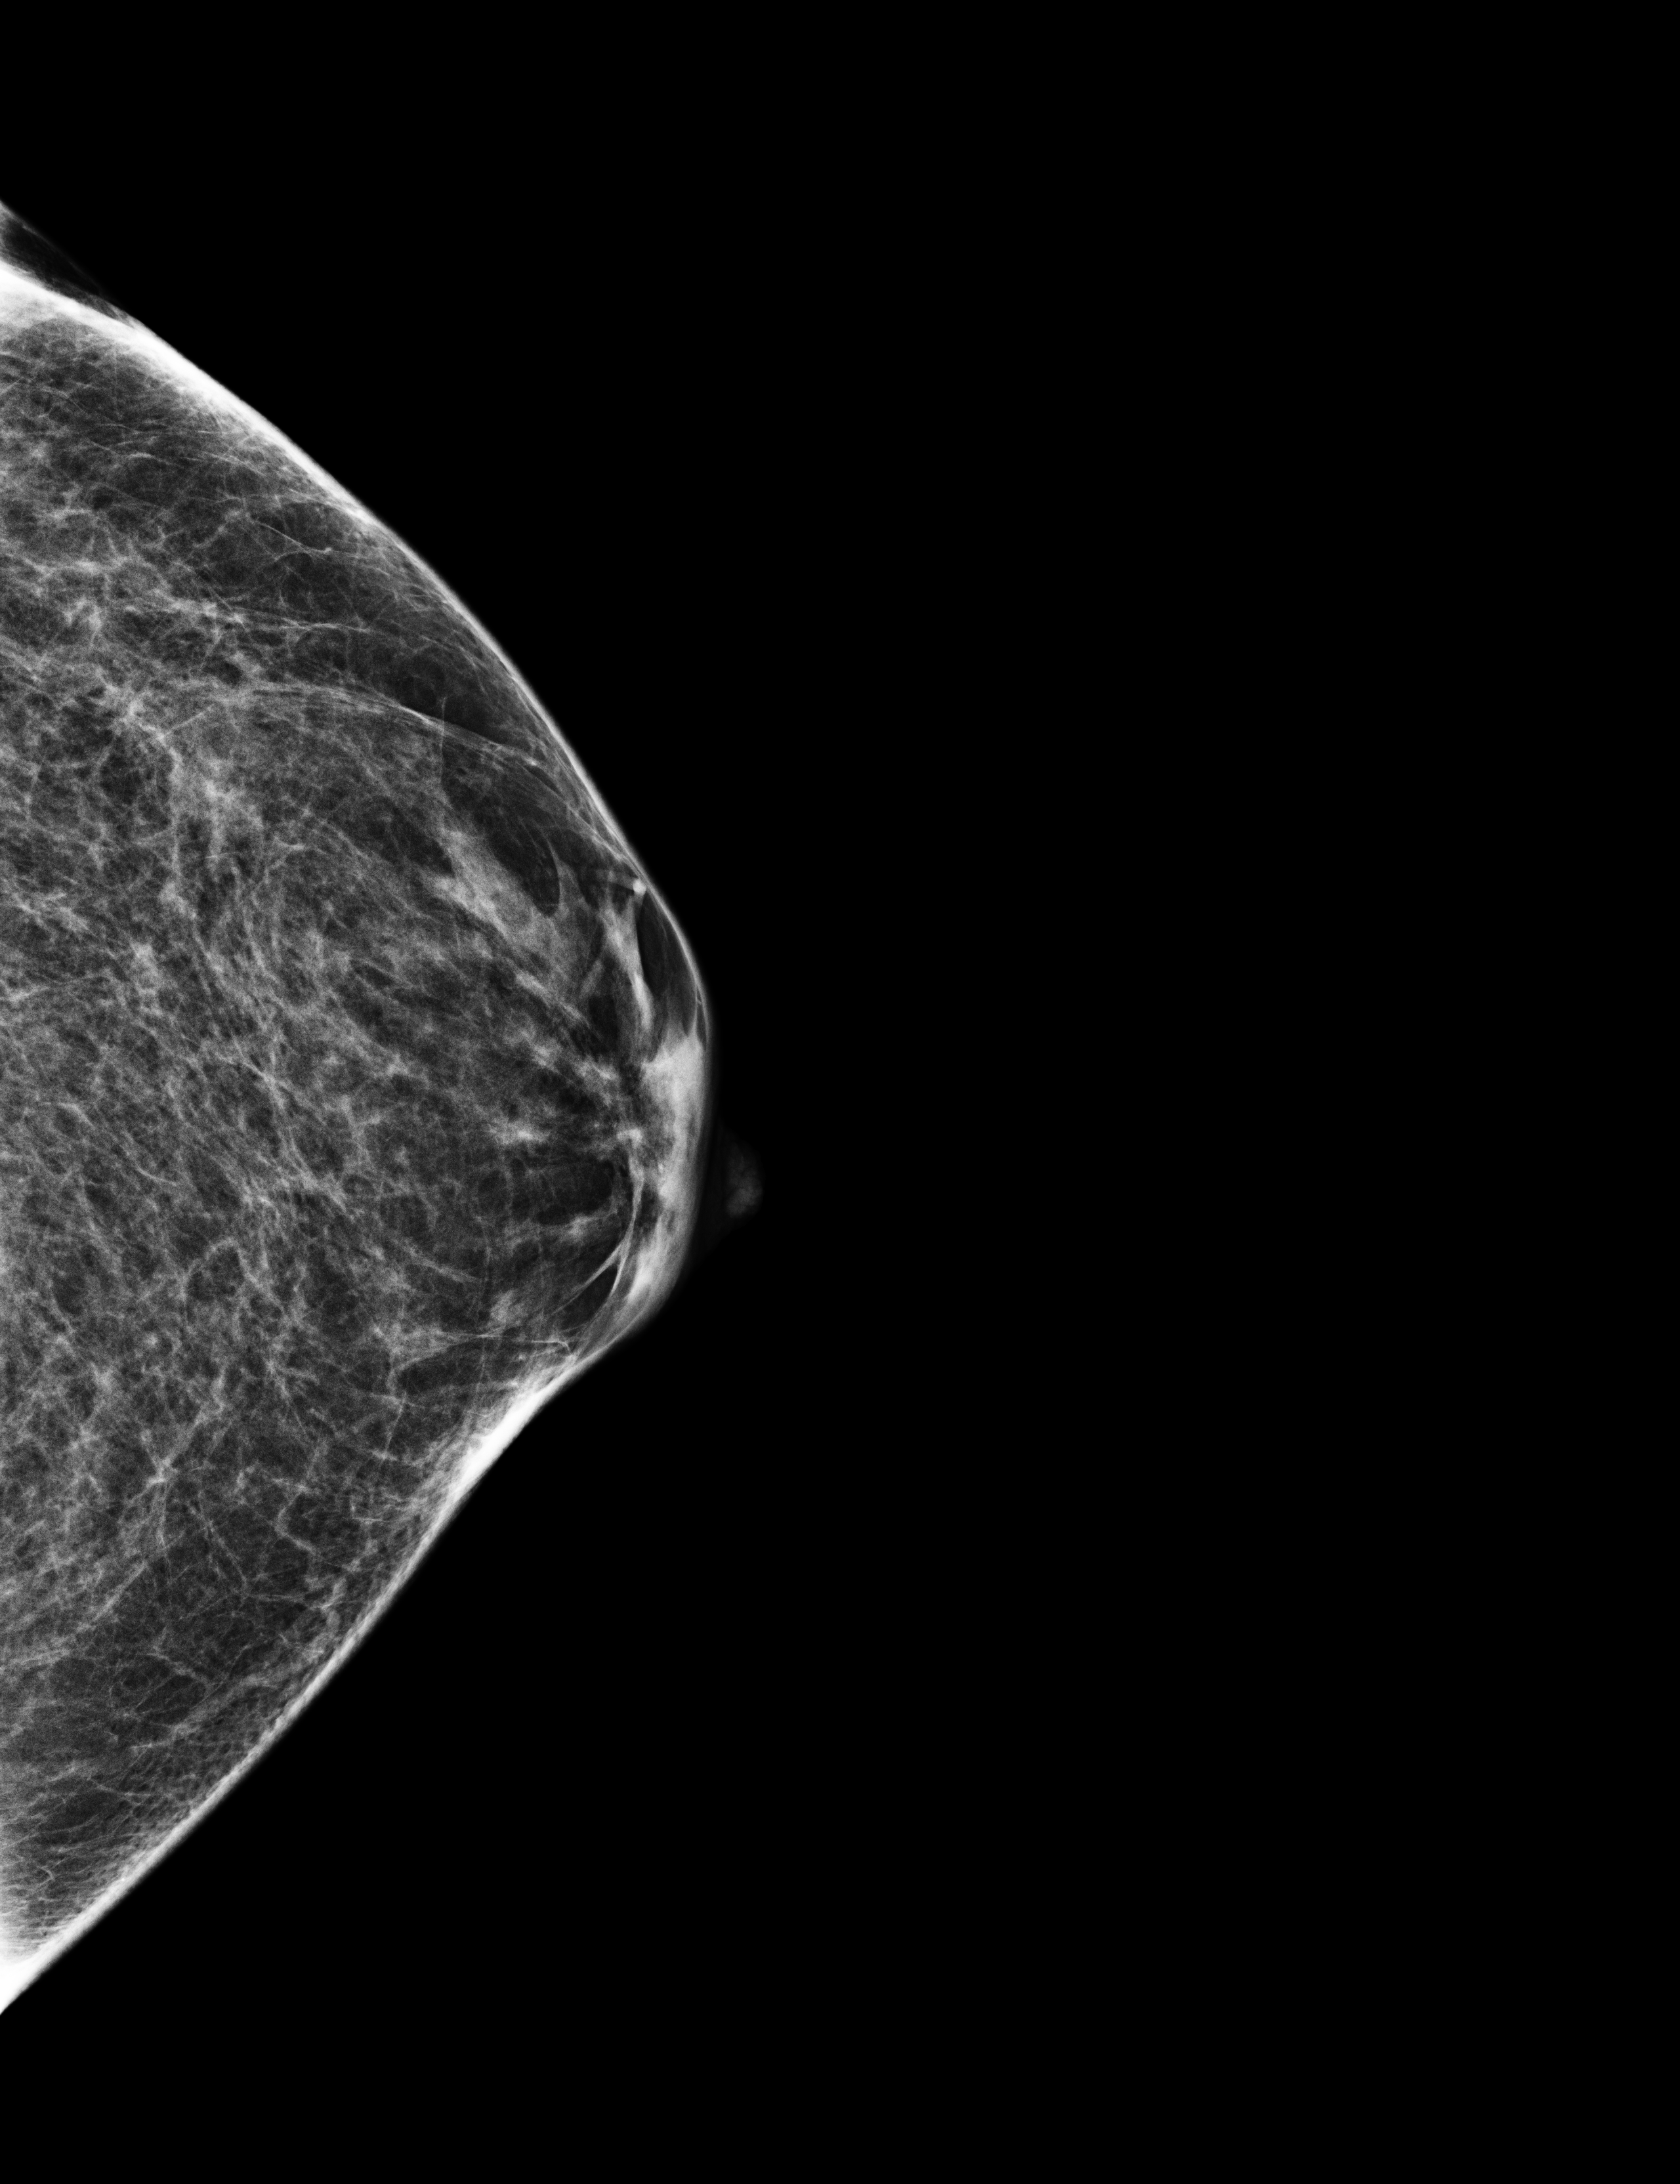
Screening examination; compressed breast thickness 51 mm. Female patient, age 52 years.
Image type: full-field digital mammogram. Breast: left. Projection: CC view.